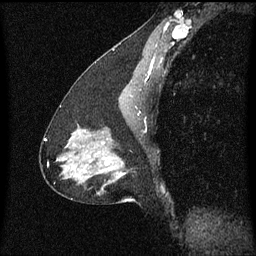
Breast MRI (dynamic contrast-enhanced), one sagittal slice; position 33 of 60 along the scan axis; dynamic contrast-enhanced series, image 2 of 3 at this slice position (ordered by acquisition); 1.5 T; TE 4.2 ms, TR 8.4 ms; 256 × 256 image matrix, field of view 200 × 200 mm. Female patient, age 47 years.
Structures marked on this image (semi-automatically segmented with operator editing):
- analysis volume of interest (the breast-tissue region the enhancement analysis was run in; not a lesion): bounding box <81,140,126,195> (left, top, right, bottom; pixels)
- tumour enhancement mask (voxels above the 70 % enhancement threshold inside the analysis volume of interest): <105,162,109,165>